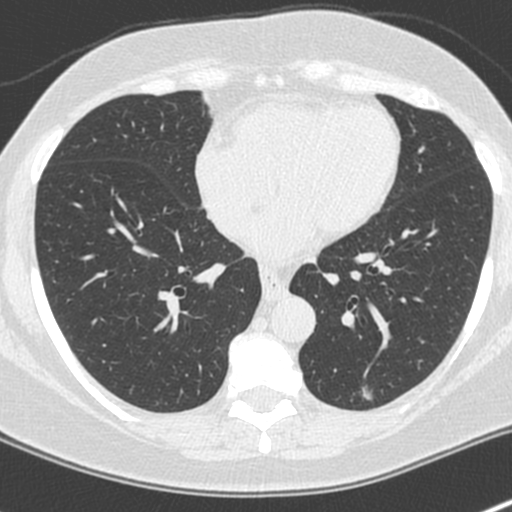
Axial slice from a low-dose chest CT screening exam, baseline screening round, lung window (W 1500 / L -600 HU), 1.3 mm slice thickness, standard (soft-tissue) reconstruction kernel (C), 512 × 512 image matrix, field of view 300 × 300 mm. Female, age 64 years at enrolment. Former smoker at enrolment.
• Lesion marked by an expert reader, bounding box (x1, y1, x2, y2) in pixels: (347, 369, 389, 417).
• Screening reader's record for this exam: no non-calcified nodule ≥4 mm recorded.
• Official screen result: negative screen, no significant abnormalities.
• Later outcome: lung cancer diagnosed 549 days after this screen — adenocarcinoma, NOS, left lower lobe, poorly differentiated (G3), stage IA (AJCC 6th edition), 8 mm at pathology.